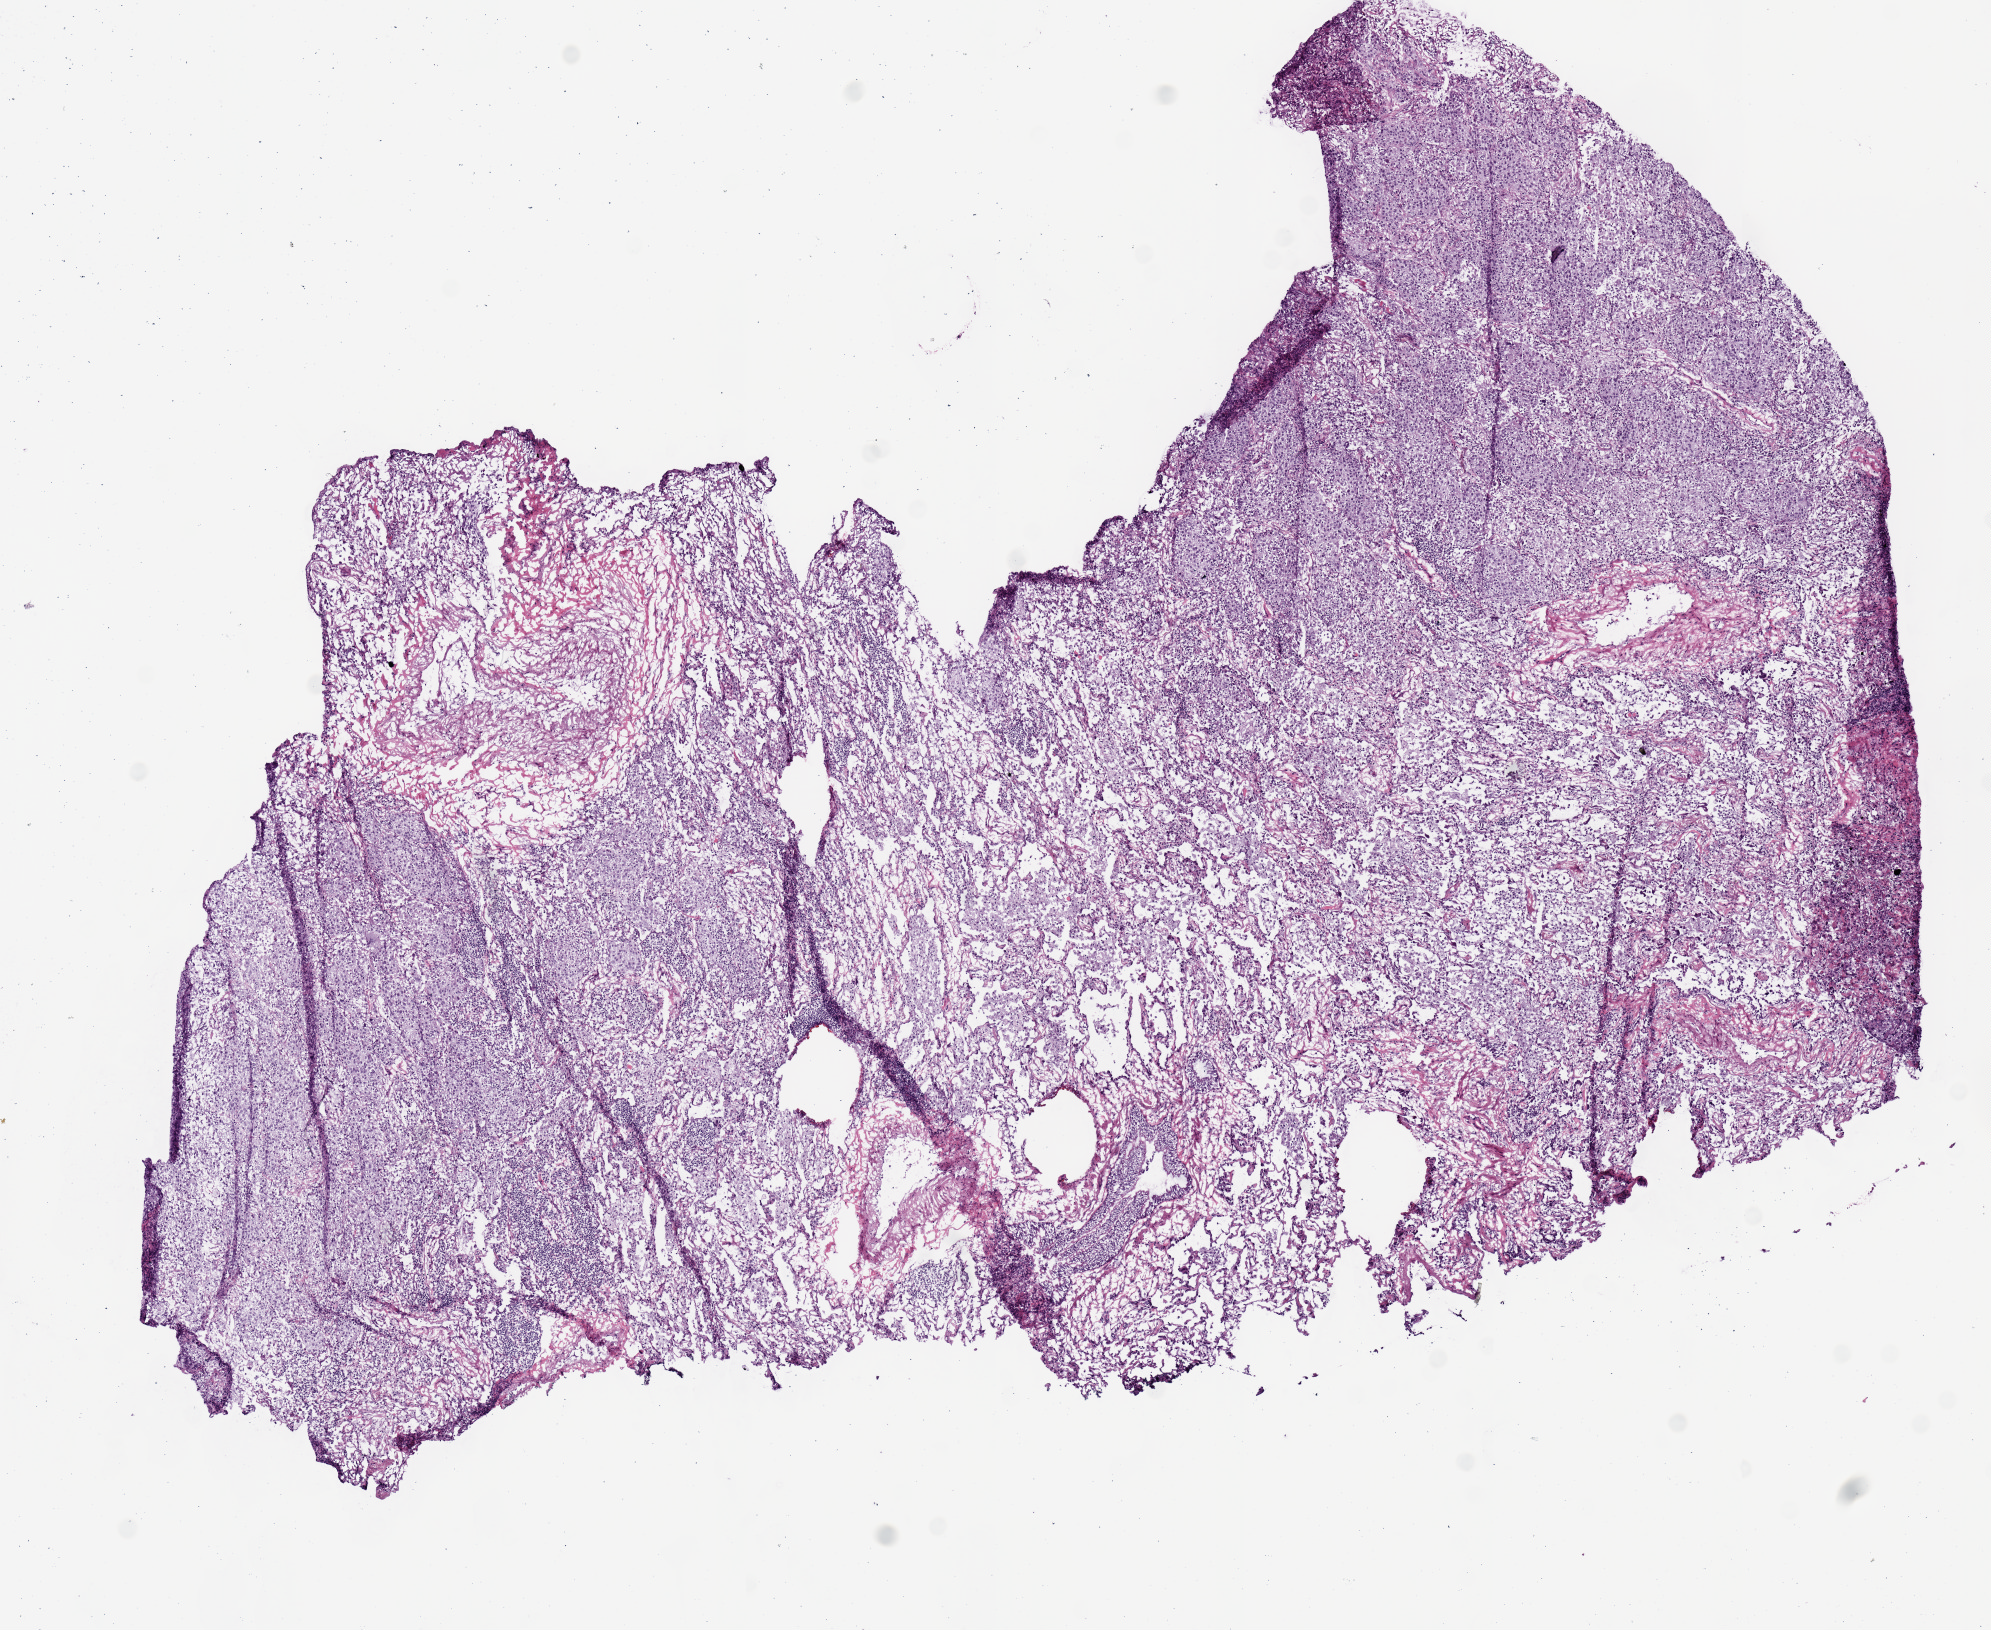
H&E whole-slide image, low-resolution overview of the scanned area, about 7.9 x 6.4 mm (from a 20x scan), frozen section from the top of the tissue portion, primary tumour sample from the lung. Patient: female, age at initial diagnosis 76 years. Pathologist review of this section (percent, as recorded): tumour cells 0%, tumour nuclei 75%, normal cells 0%, stromal cells 0%, necrosis 2%.
AJCC pathologic stage: IIA (7th edition). TNM: T2b N0 M0. Pathologic diagnosis: Adenocarcinoma, NOS (lower lobe, lung). Laterality: right.